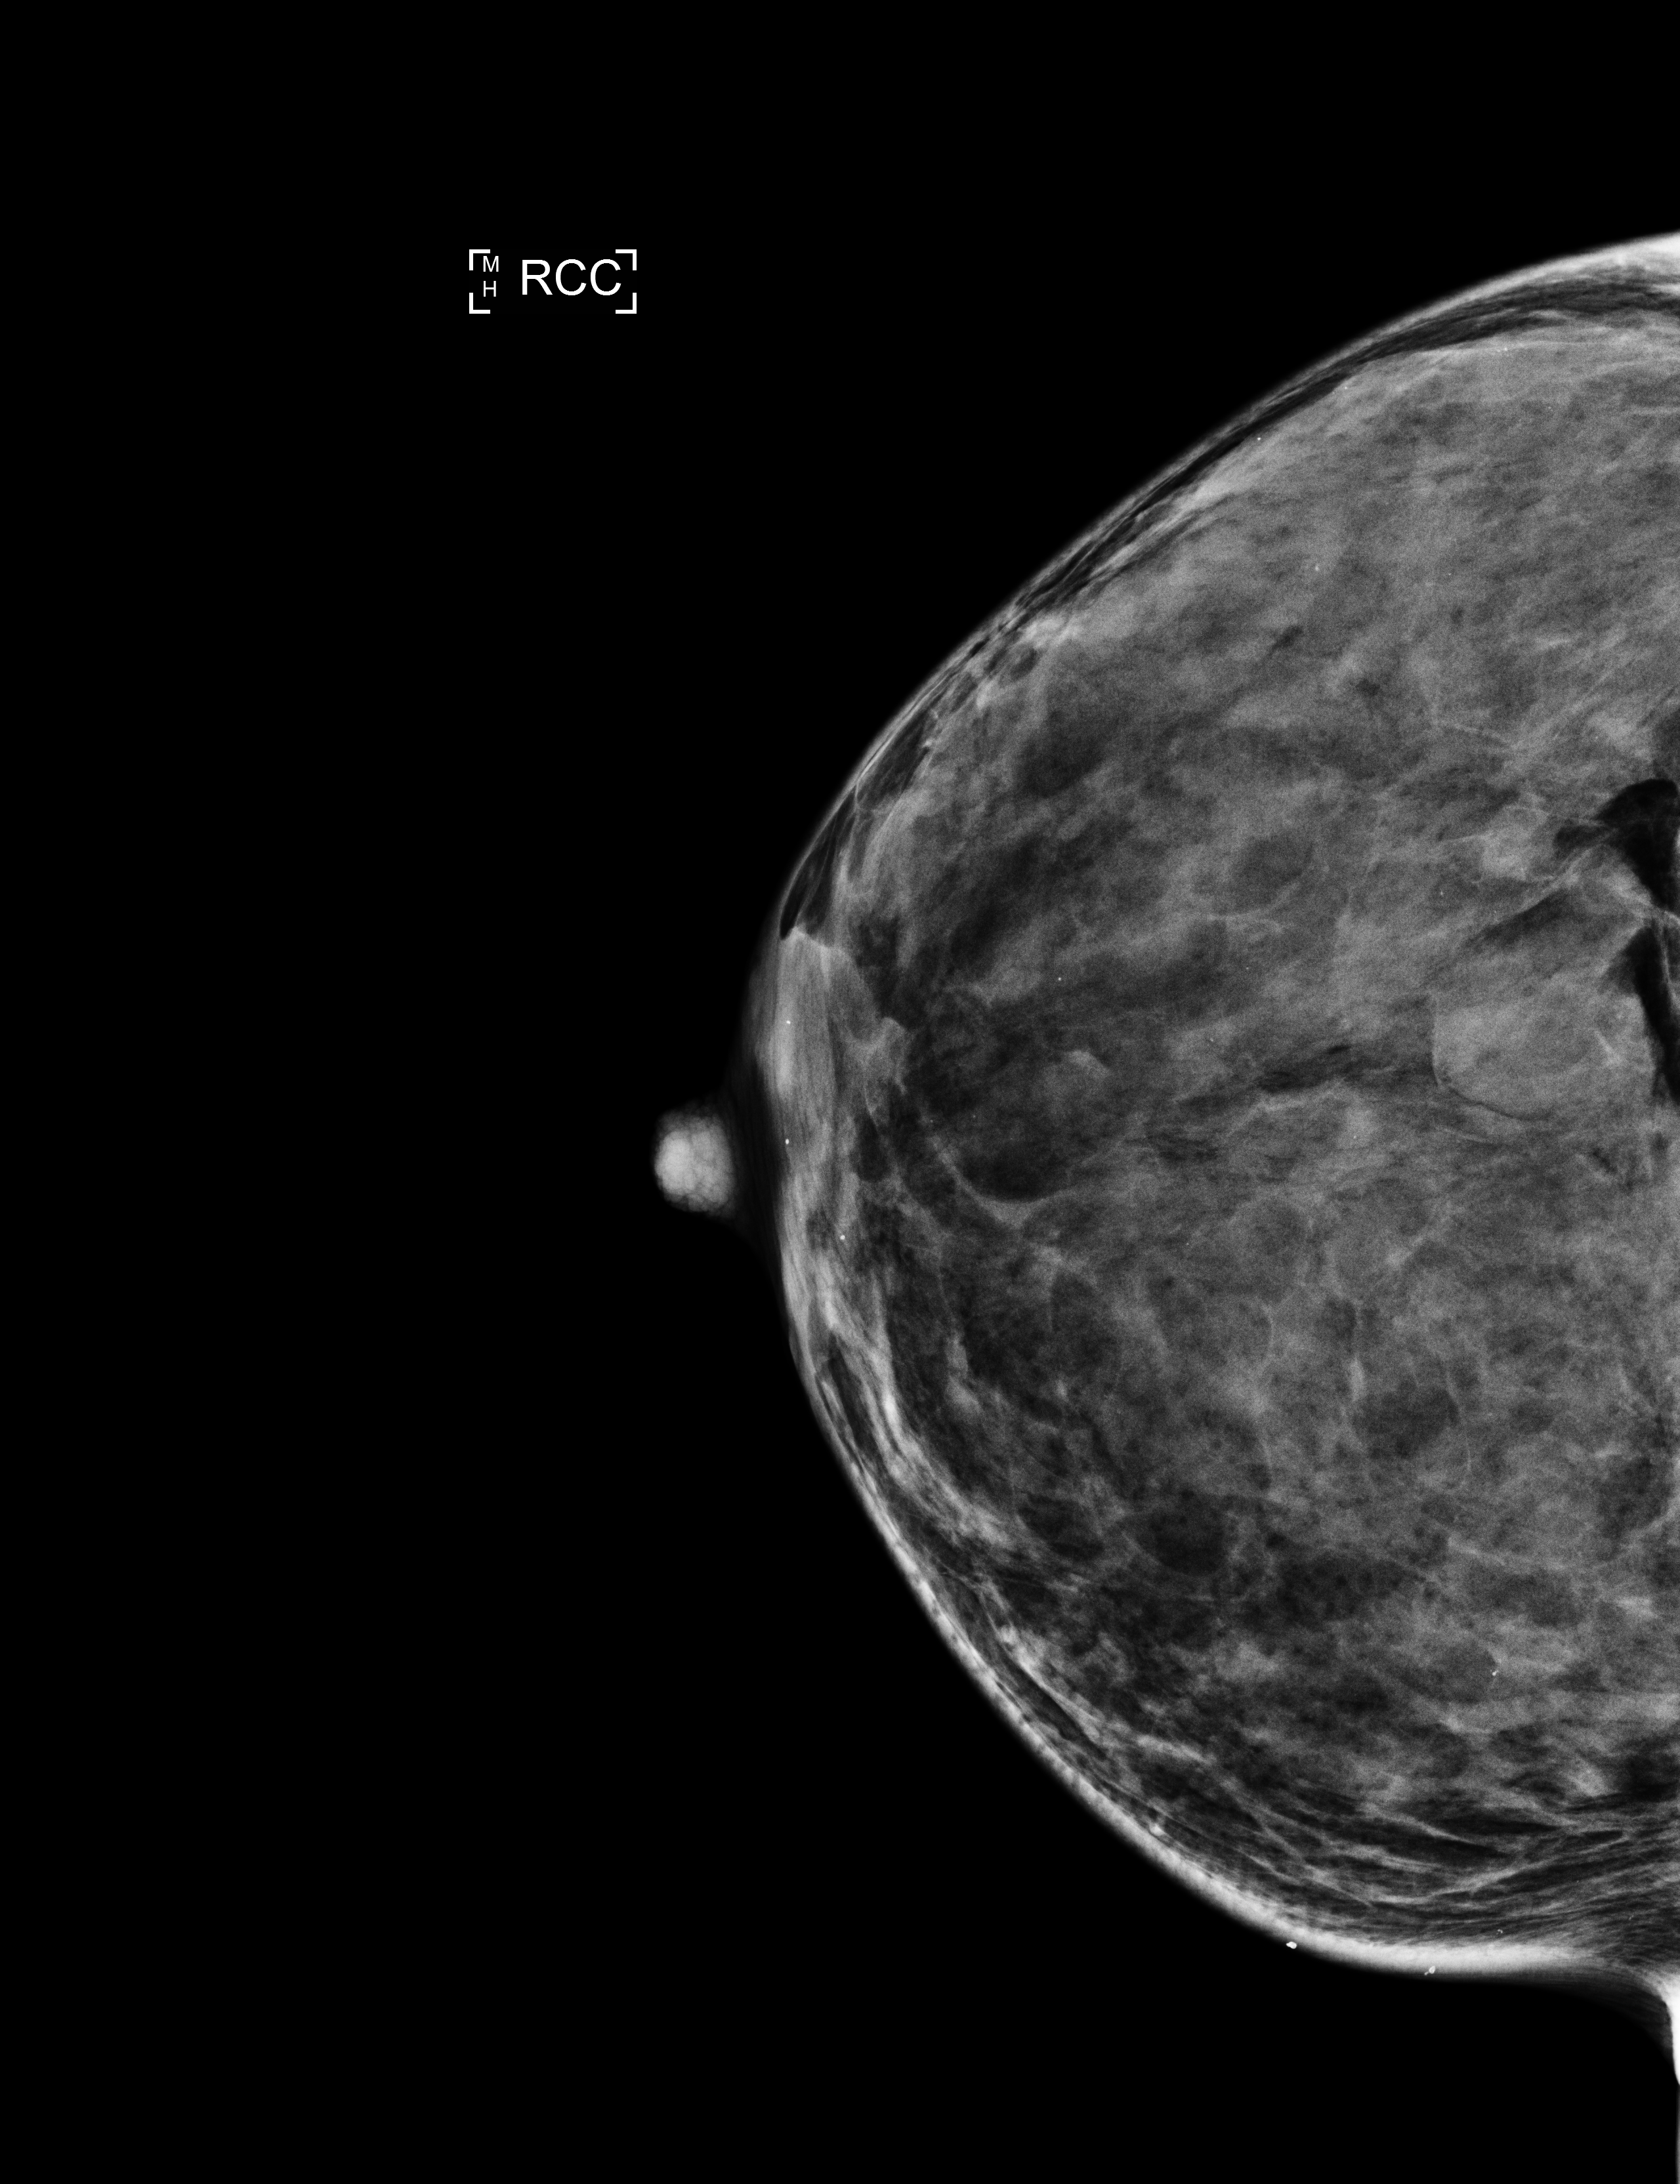
Annual screening mammography examination. Patient aged 42 years (female).
Image type: full-field digital mammogram. Breast: right. Projection: CC view.